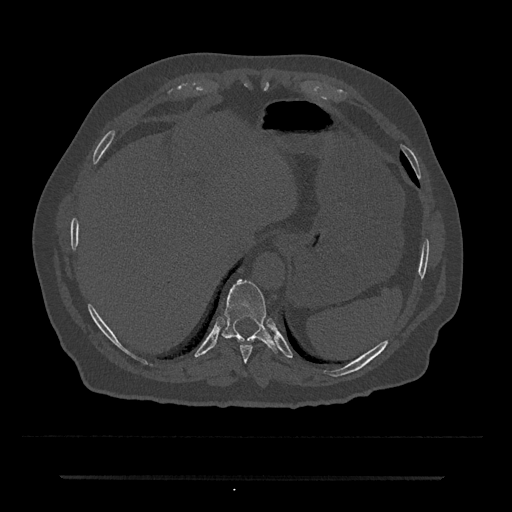
CT including the spine, one axial slice; slice 244 of 797 in the series (ordered by position); bone window (W 1800 / L 400 HU); 0.5 mm slice thickness; 512 × 512 image matrix. Patient: male, 69 years. Case-level facts recorded for this patient, not image findings: primary cancer: prostate.
Structures marked on this image (semi-automatically segmented with operator editing):
- T10 vertebra: box from (x=222, y=279) to (x=278, y=353) px
- T9 vertebra: (x=240, y=345)–(x=253, y=364)